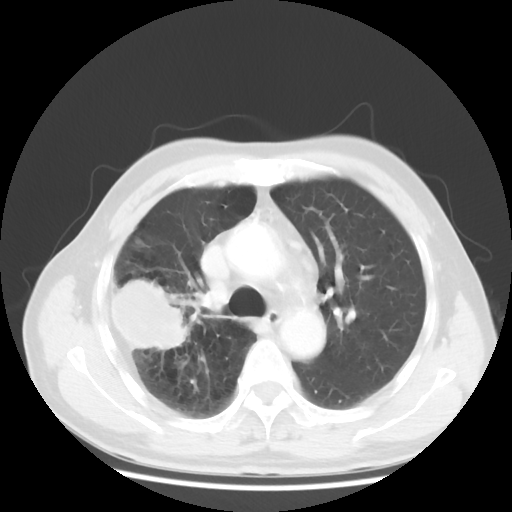
Chest CT, one axial slice; reconstruction kernel STANDARD; lung window (W 1500 / L -600 HU); 5 mm slice thickness; 512 × 512 image matrix, field of view 360 × 360 mm. Patient: male, 69 years. From the clinical record (not read from this slice): clinical TNM (as recorded): T3 N0 M0.
Structures marked on this image (bounding box drawn by a radiologist):
- lung tumour (recorded histology: adenocarcinoma): bounding box [x1, y1, x2, y2] px = [108, 272, 188, 352]